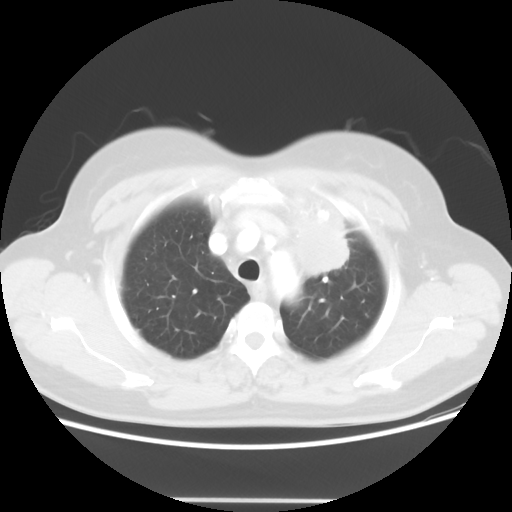
Chest CT, one axial slice. Position 44 of 52 along the scan axis. Lung window (W 1500 / L -600 HU). 512 × 512 image matrix, field of view 382 × 382 mm. Female patient, age 52 years. From the clinical record (not read from this slice): clinical TNM (as recorded): T2 N3 M0.
Annotated regions visible in this slice (rectangle marked by the reading radiologist):
- lung tumour (recorded histology: adenocarcinoma): bounding box <287,197,353,277> (left, top, right, bottom; pixels)